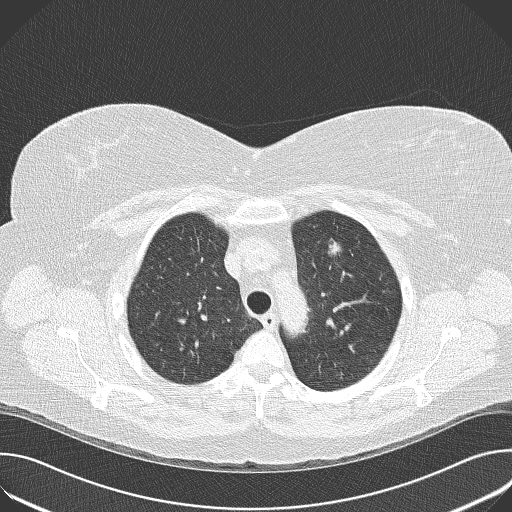
Axial slice from a low-dose chest CT screening exam; baseline annual screen; lung window (W 1500 / L -600 HU); 2 mm slice thickness; lung (sharp) reconstruction kernel (B50f); slice 113 of 143 in the series. Female, age 57 years at enrolment.
Expert-annotated lung lesion, bounding box (x1, y1, x2, y2) in pixels: (316, 235, 350, 271). The screening reader recorded 3 non-calcified nodules or masses ≥4 mm on this exam (lingula, right middle lobe, left upper lobe); which of them this box marks is not recorded. Later outcome: lung cancer diagnosed 446 days after this screen — adenocarcinoma, NOS, left upper lobe, poorly differentiated (G3), stage IA (AJCC 6th edition), 24 mm at pathology.